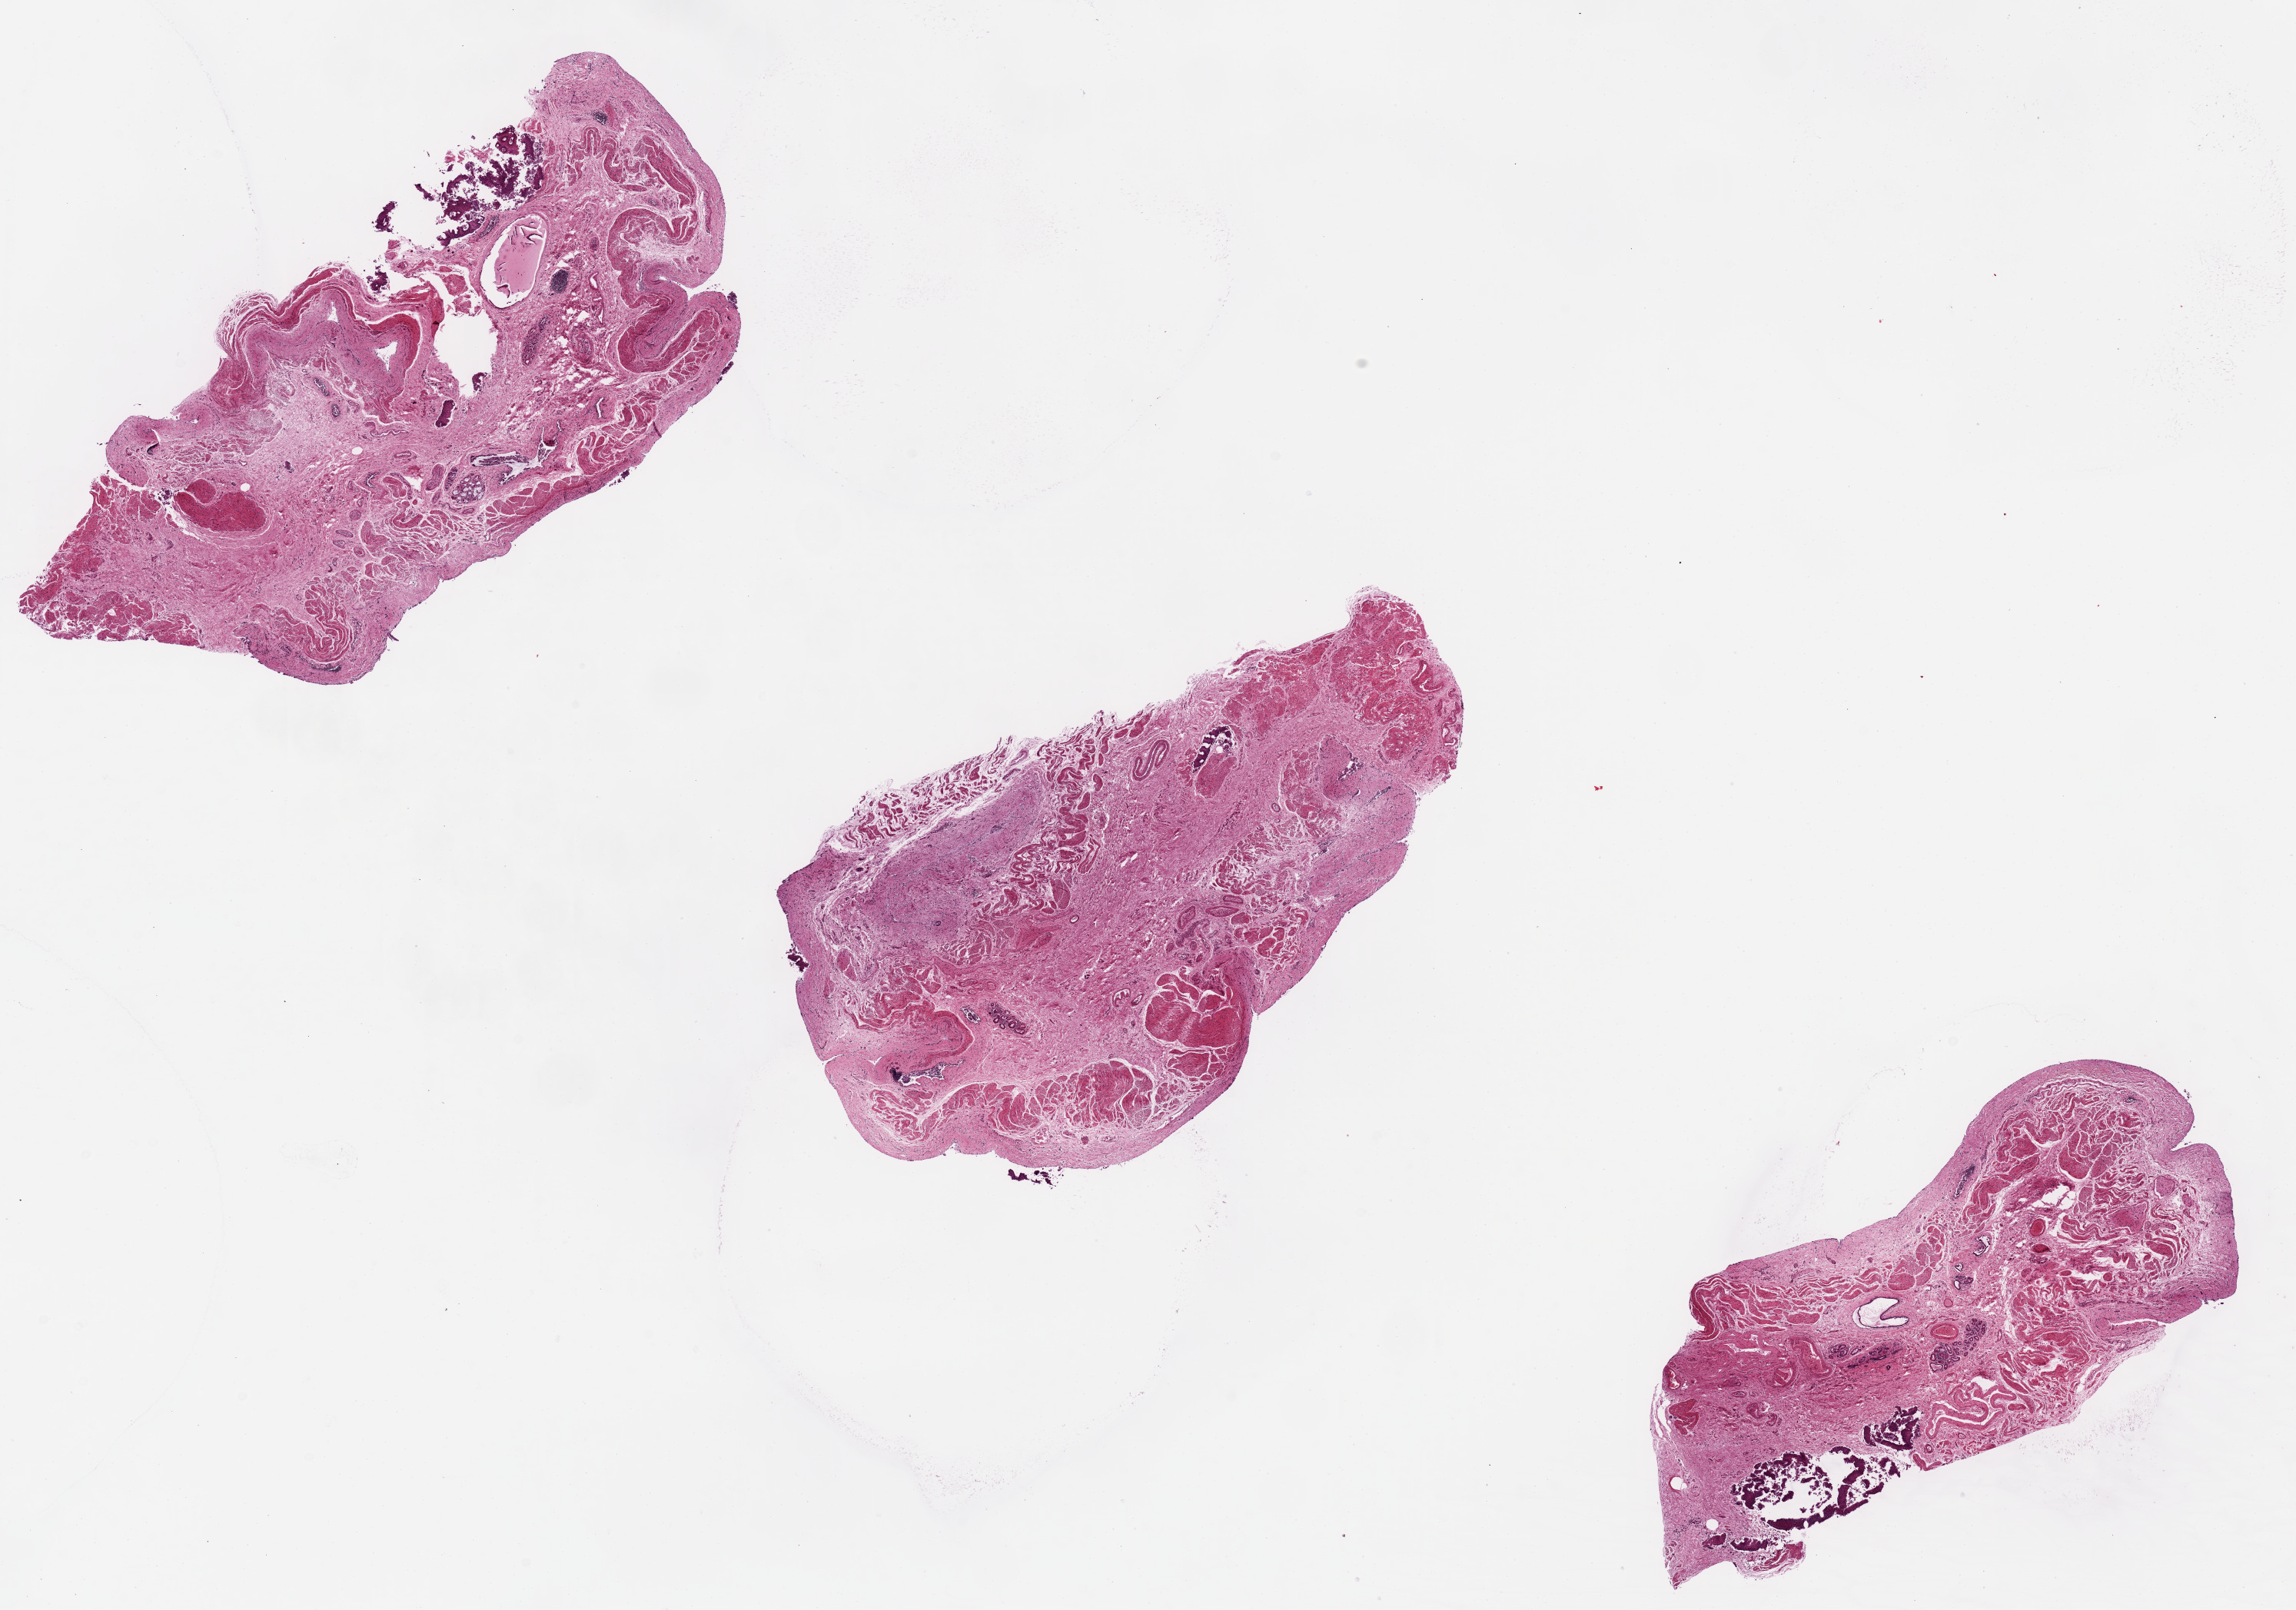
Digitized haematoxylin and eosin-stained section — low-resolution overview of the scanned area, about 23.6 x 16.6 mm (slide scanned at 20x); PAXgene-fixed, paraffin-embedded tissue; section of esophageal mucous membrane (target tissue); tissue donor sample. Female donor.
Review note (as recorded): No mucosa present other than 2 microfoci. (See Request).